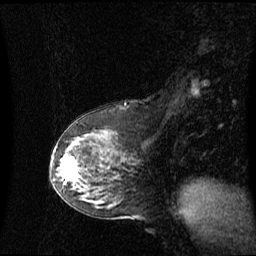
Breast MRI (dynamic contrast-enhanced), one sagittal slice; slice 33 of 60 in the series (ordered by position); dynamic contrast-enhanced series, image 2 of 3 at this slice position (ordered by acquisition); 1.5 T; TE 4.2 ms, TR 8.4 ms; 2.1 mm slice thickness; 256 × 256 image matrix, field of view 260 × 260 mm. Patient: female, 59 years. From the clinical record (not read from this slice): setting: breast cancer imaged before/during neoadjuvant chemotherapy; receptor status: HR-positive, HER2-negative.
Annotated regions visible in this slice (semi-automatic segmentation, software-assisted and operator-edited):
- analysis volume of interest (the breast-tissue region the enhancement analysis was run in; not a lesion): bounding box (x1, y1, x2, y2) in pixels: (58, 148, 88, 191)
- tumour enhancement mask (voxels above the 70 % enhancement threshold inside the analysis volume of interest): (65, 162, 79, 180)